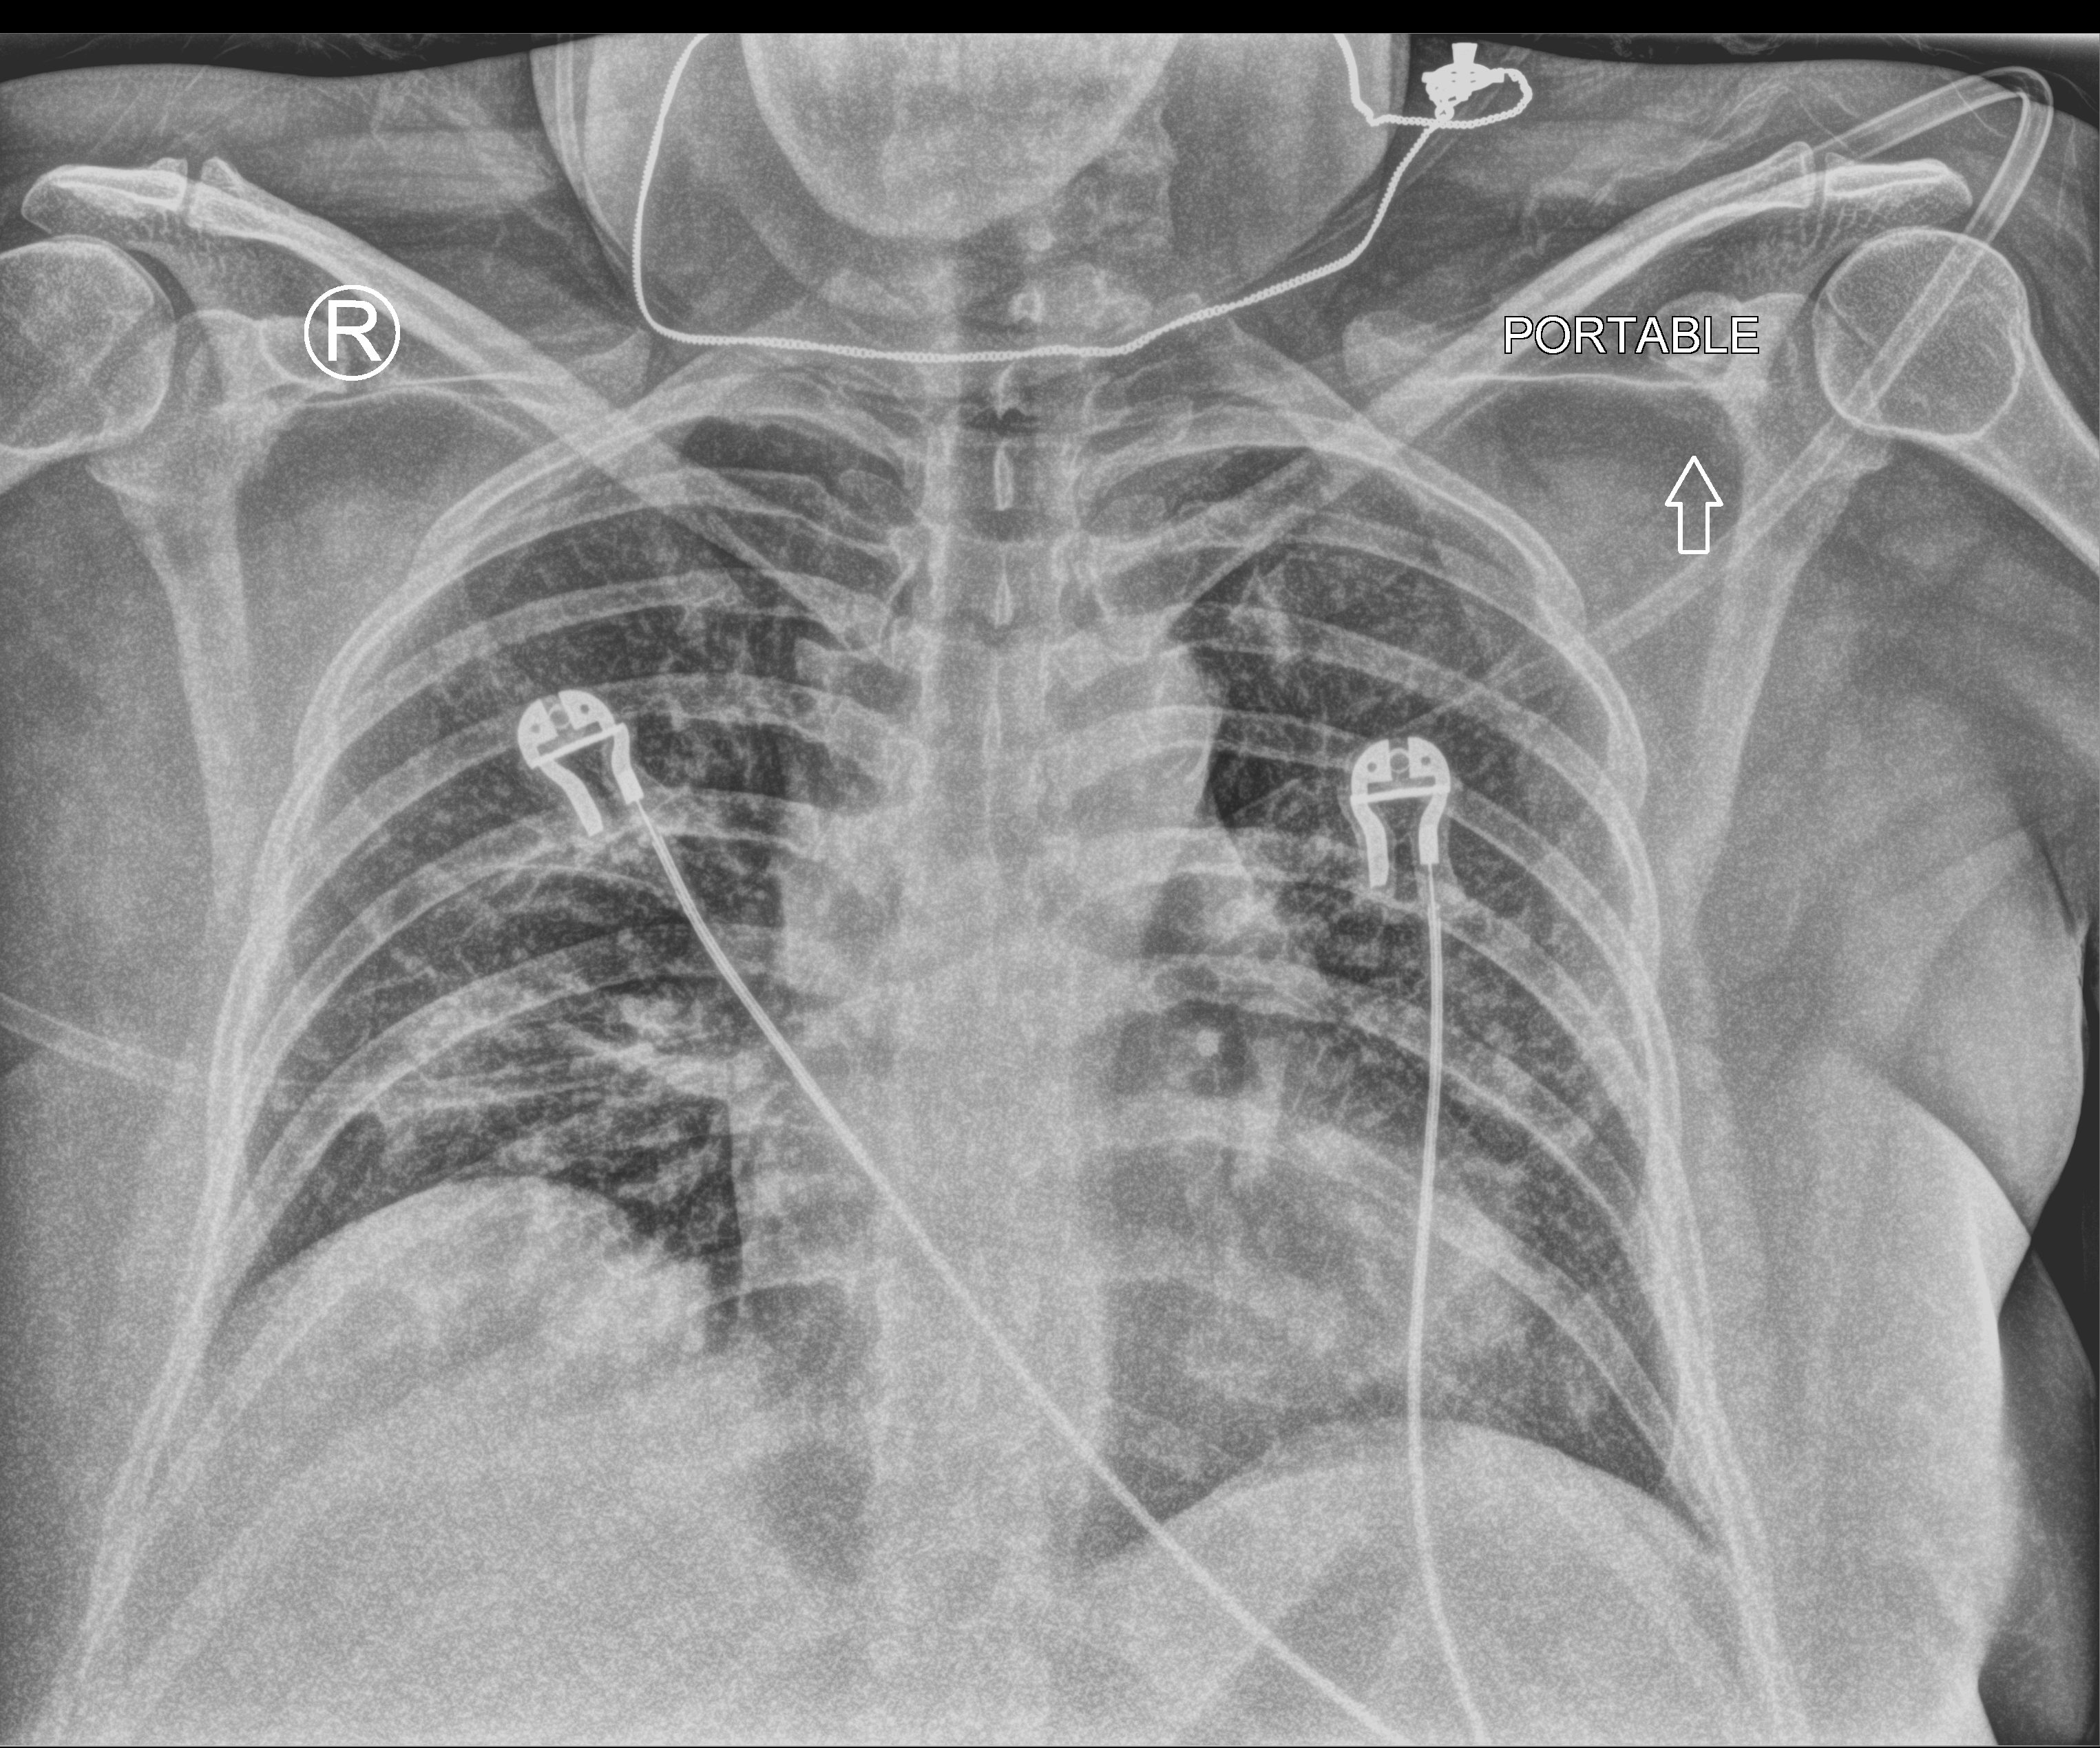
Bedside chest radiograph (computed radiography). Patient hospitalised with COVID-19; female, aged 18–59 years.
Admission-level facts for this patient (not findings on this image; timing relative to this image not recorded): other chronic lung disease (admission record): yes.